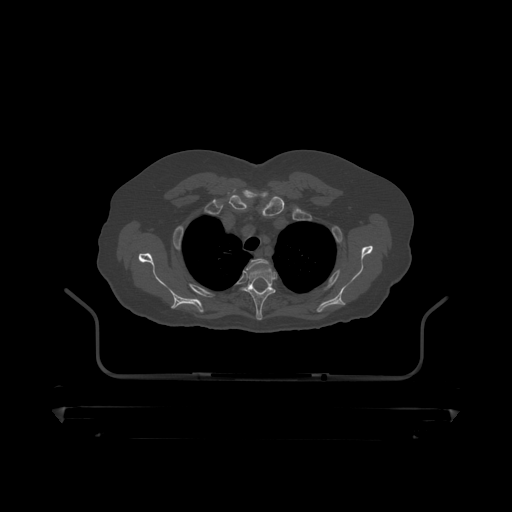
CT including the spine, one axial slice; position 358 of 390 along the scan axis; 120 kVp; bone window (W 1800 / L 400 HU); 1.25 mm slice thickness; 512 × 512 image matrix. Male patient, age 60 years. Case-level facts recorded for this patient, not image findings: primary cancer: prostate.
Structures marked on this image (semi-automatic segmentation, software-assisted and operator-edited):
- T2 vertebra: box from (x=247, y=259) to (x=267, y=270) px
- T3 vertebra: (x=244, y=262)–(x=276, y=319)